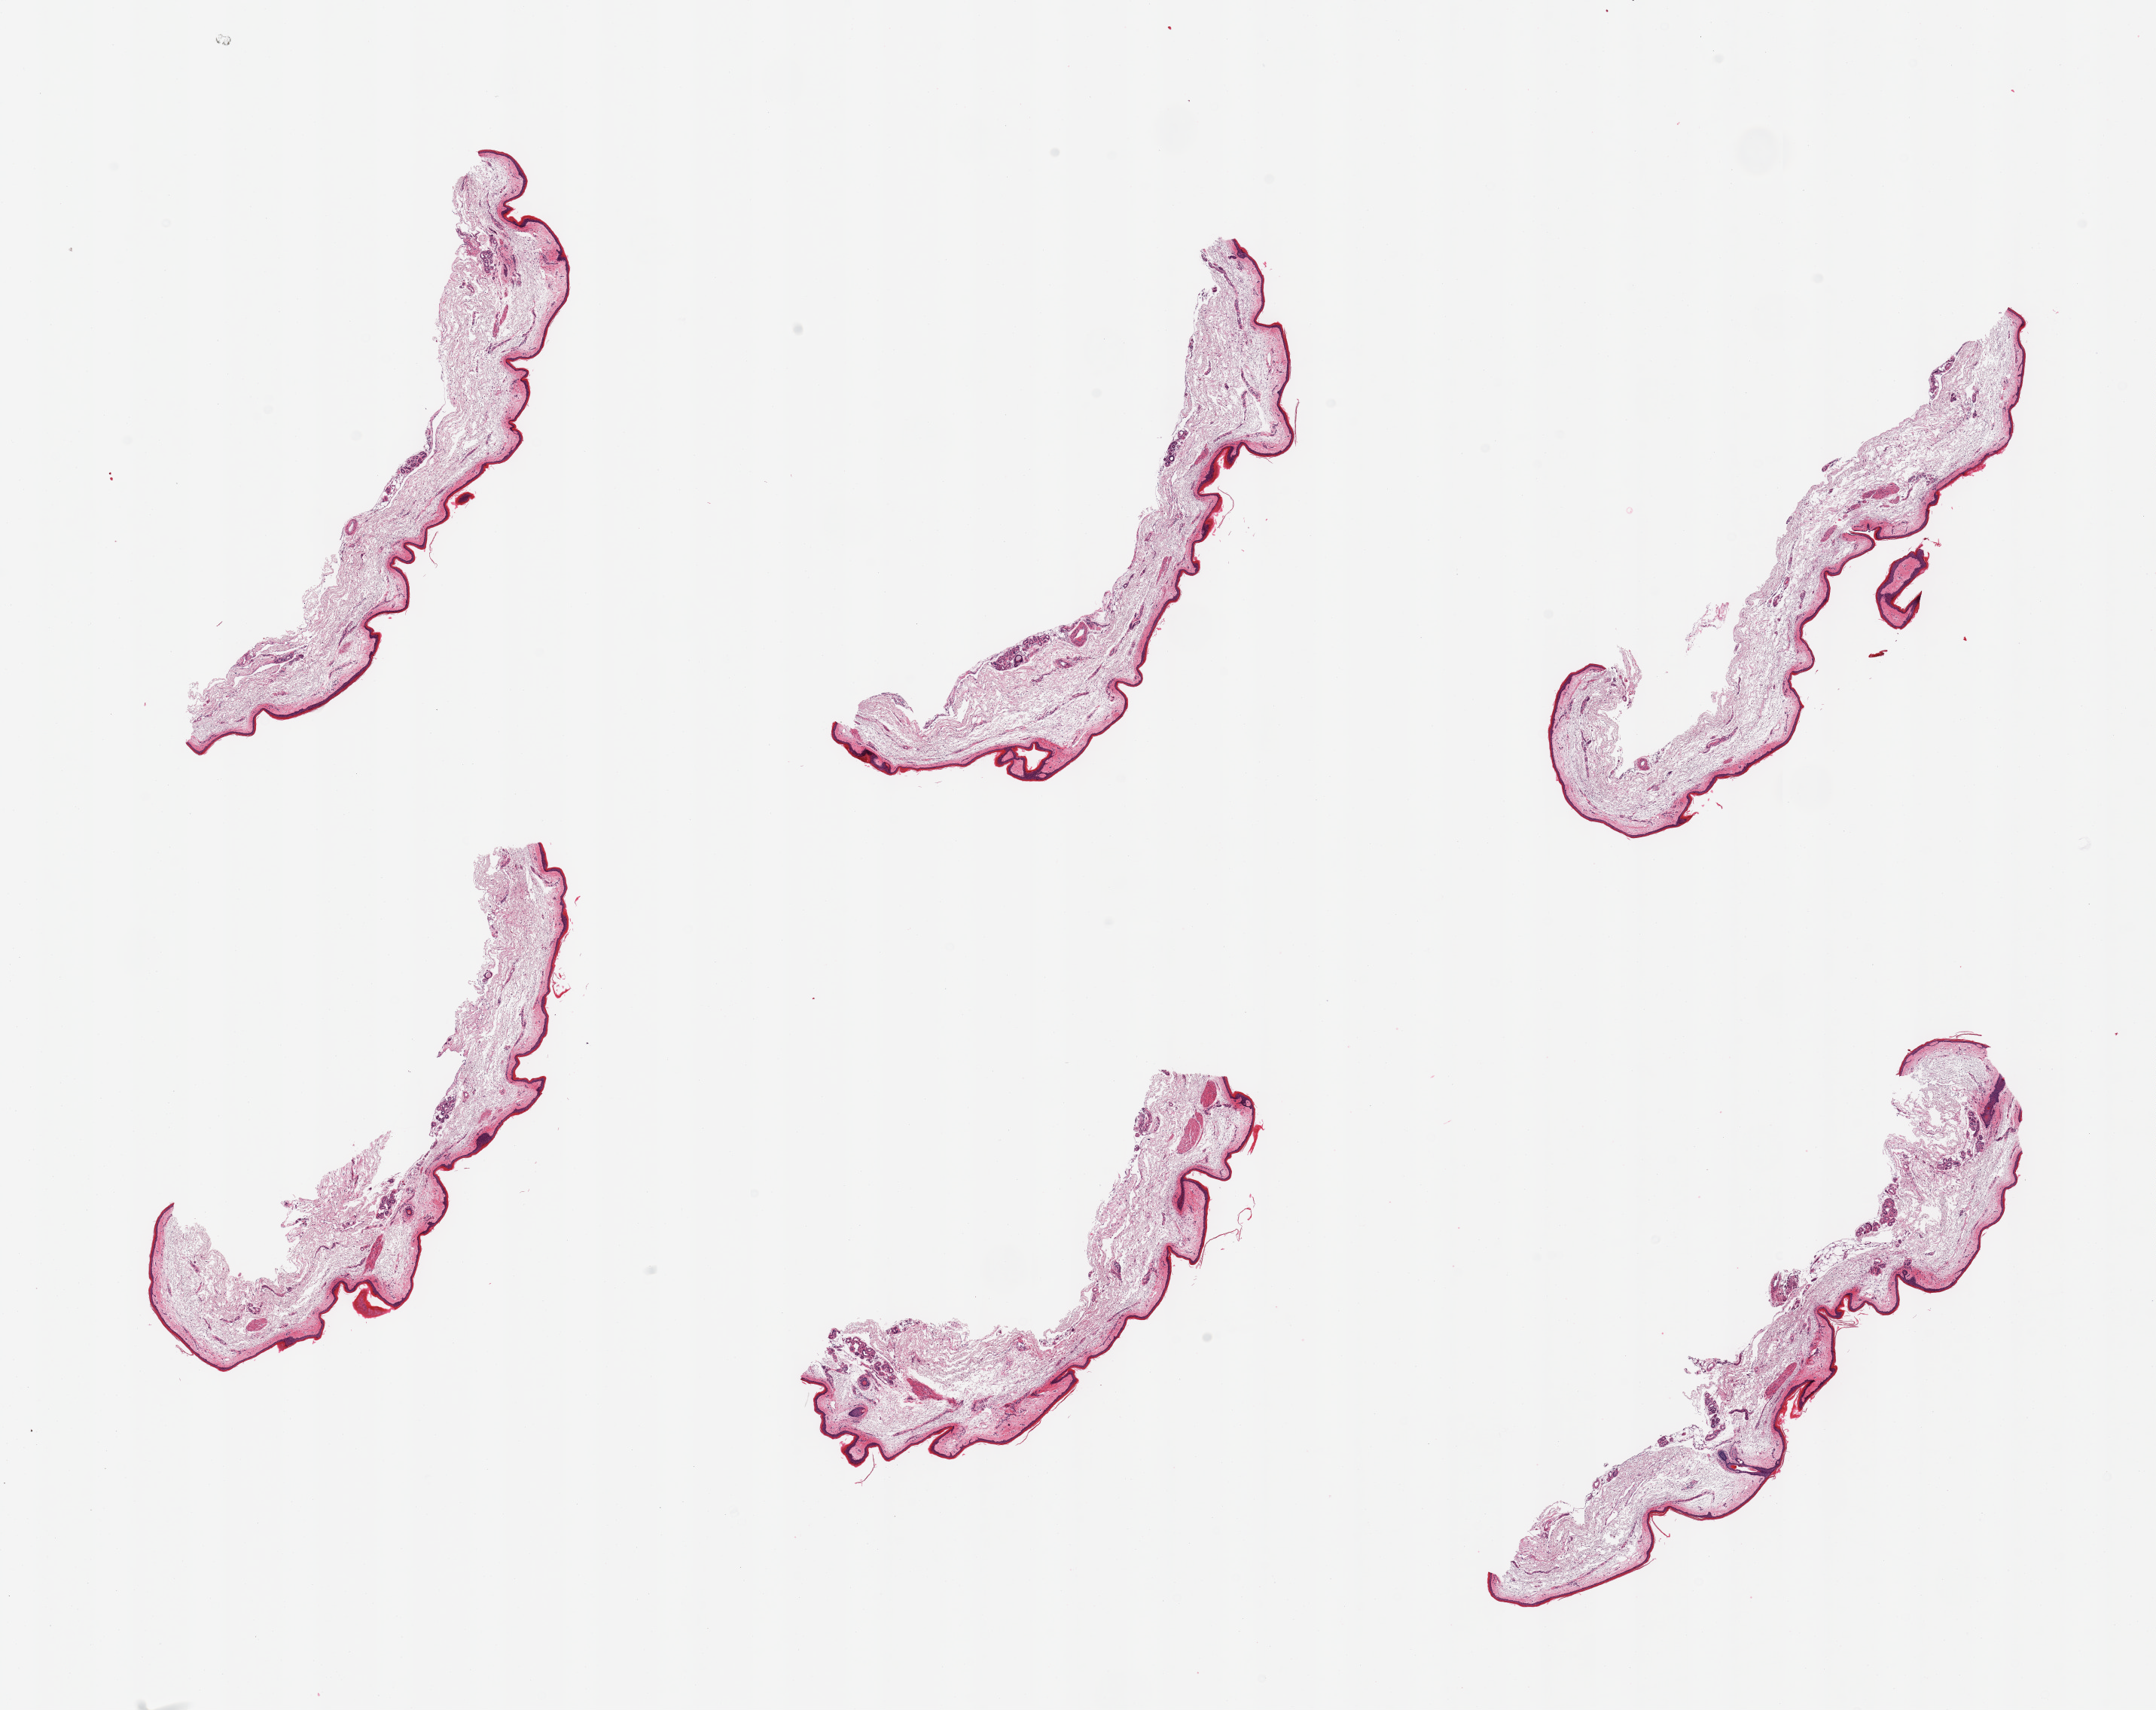
H&E whole-slide image, shown as a low-resolution overview of the whole scanned area (about 22.6 x 18.0 mm, from a 20x scan), PAXgene-fixed paraffin-embedded (PFPE) section, target tissue: skin of lower leg, tissue donor sample. Donor sex: female.
* review note (as recorded): 6 pieces; atrophic and edematous; well trimmed